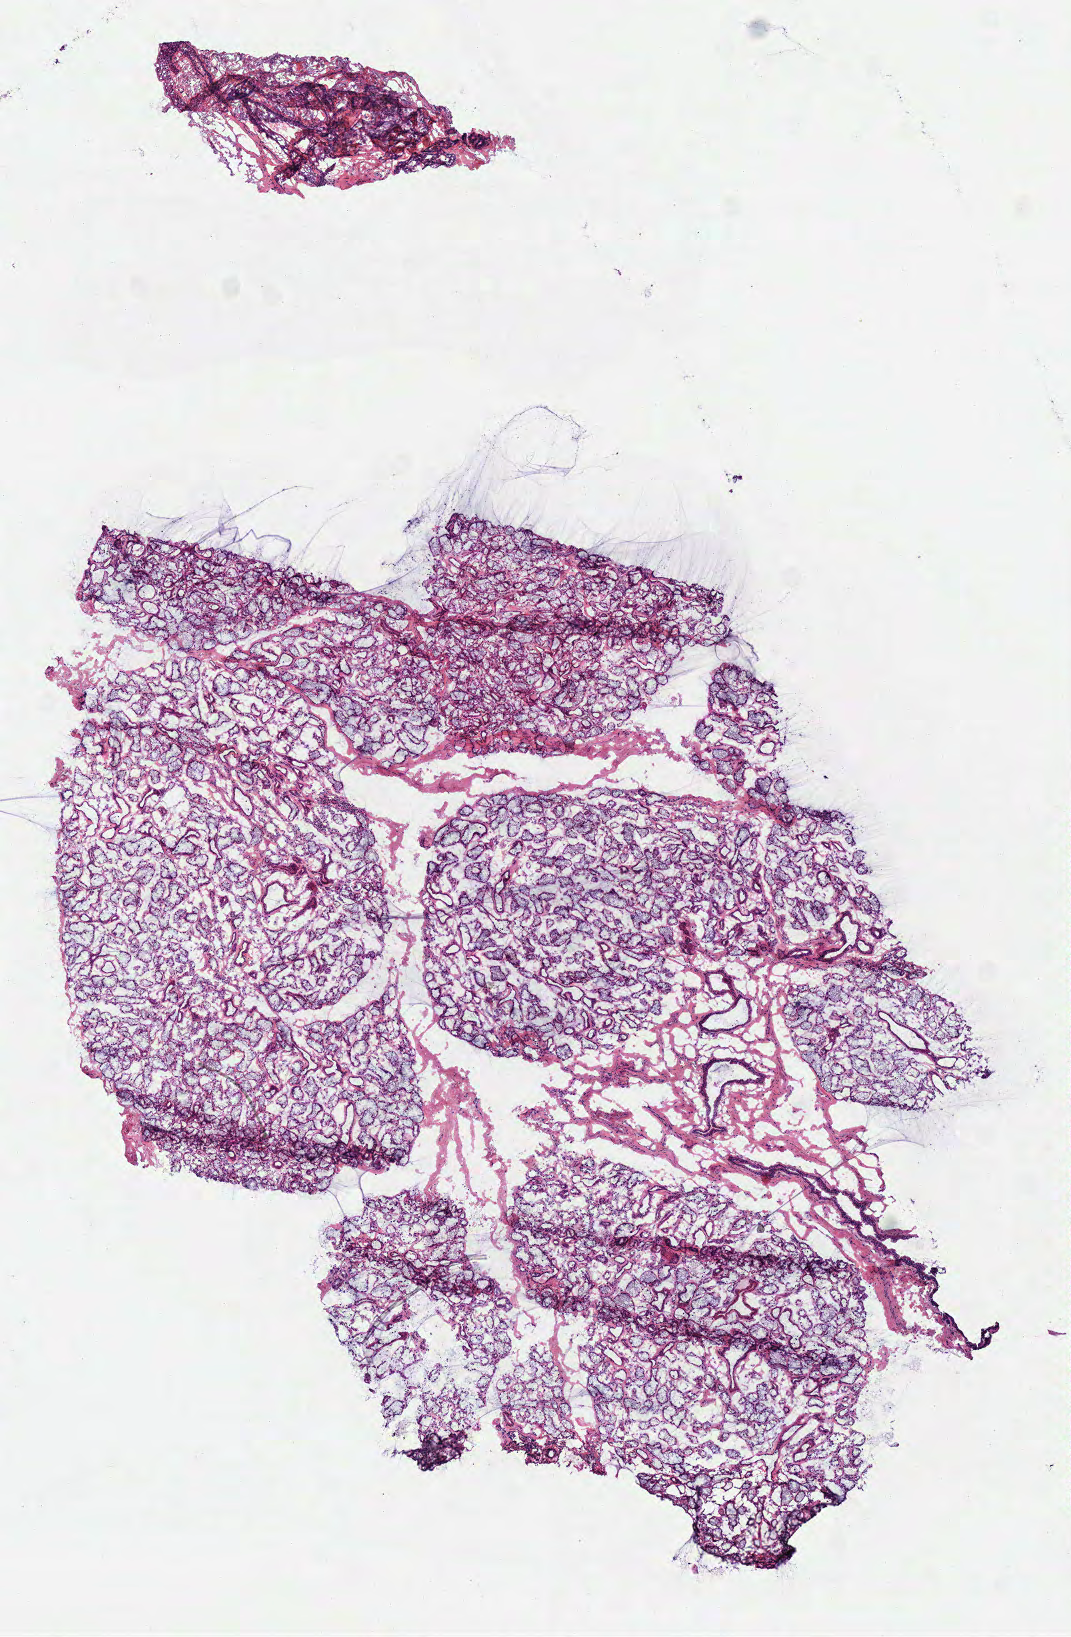
Digitized H&E tissue section (whole slide) — shown as a low-resolution overview of the whole scanned area (about 4.2 x 6.4 mm). Frozen section from the top of the tissue portion. Head and neck, solid tissue normal (non-tumour tissue) sample. Female, age 64 years at initial diagnosis.
This section: solid tissue normal sample (biorepository sample class). Patient diagnosis: Squamous cell carcinoma, NOS (overlapping lesion of lip, oral cavity and pharynx).